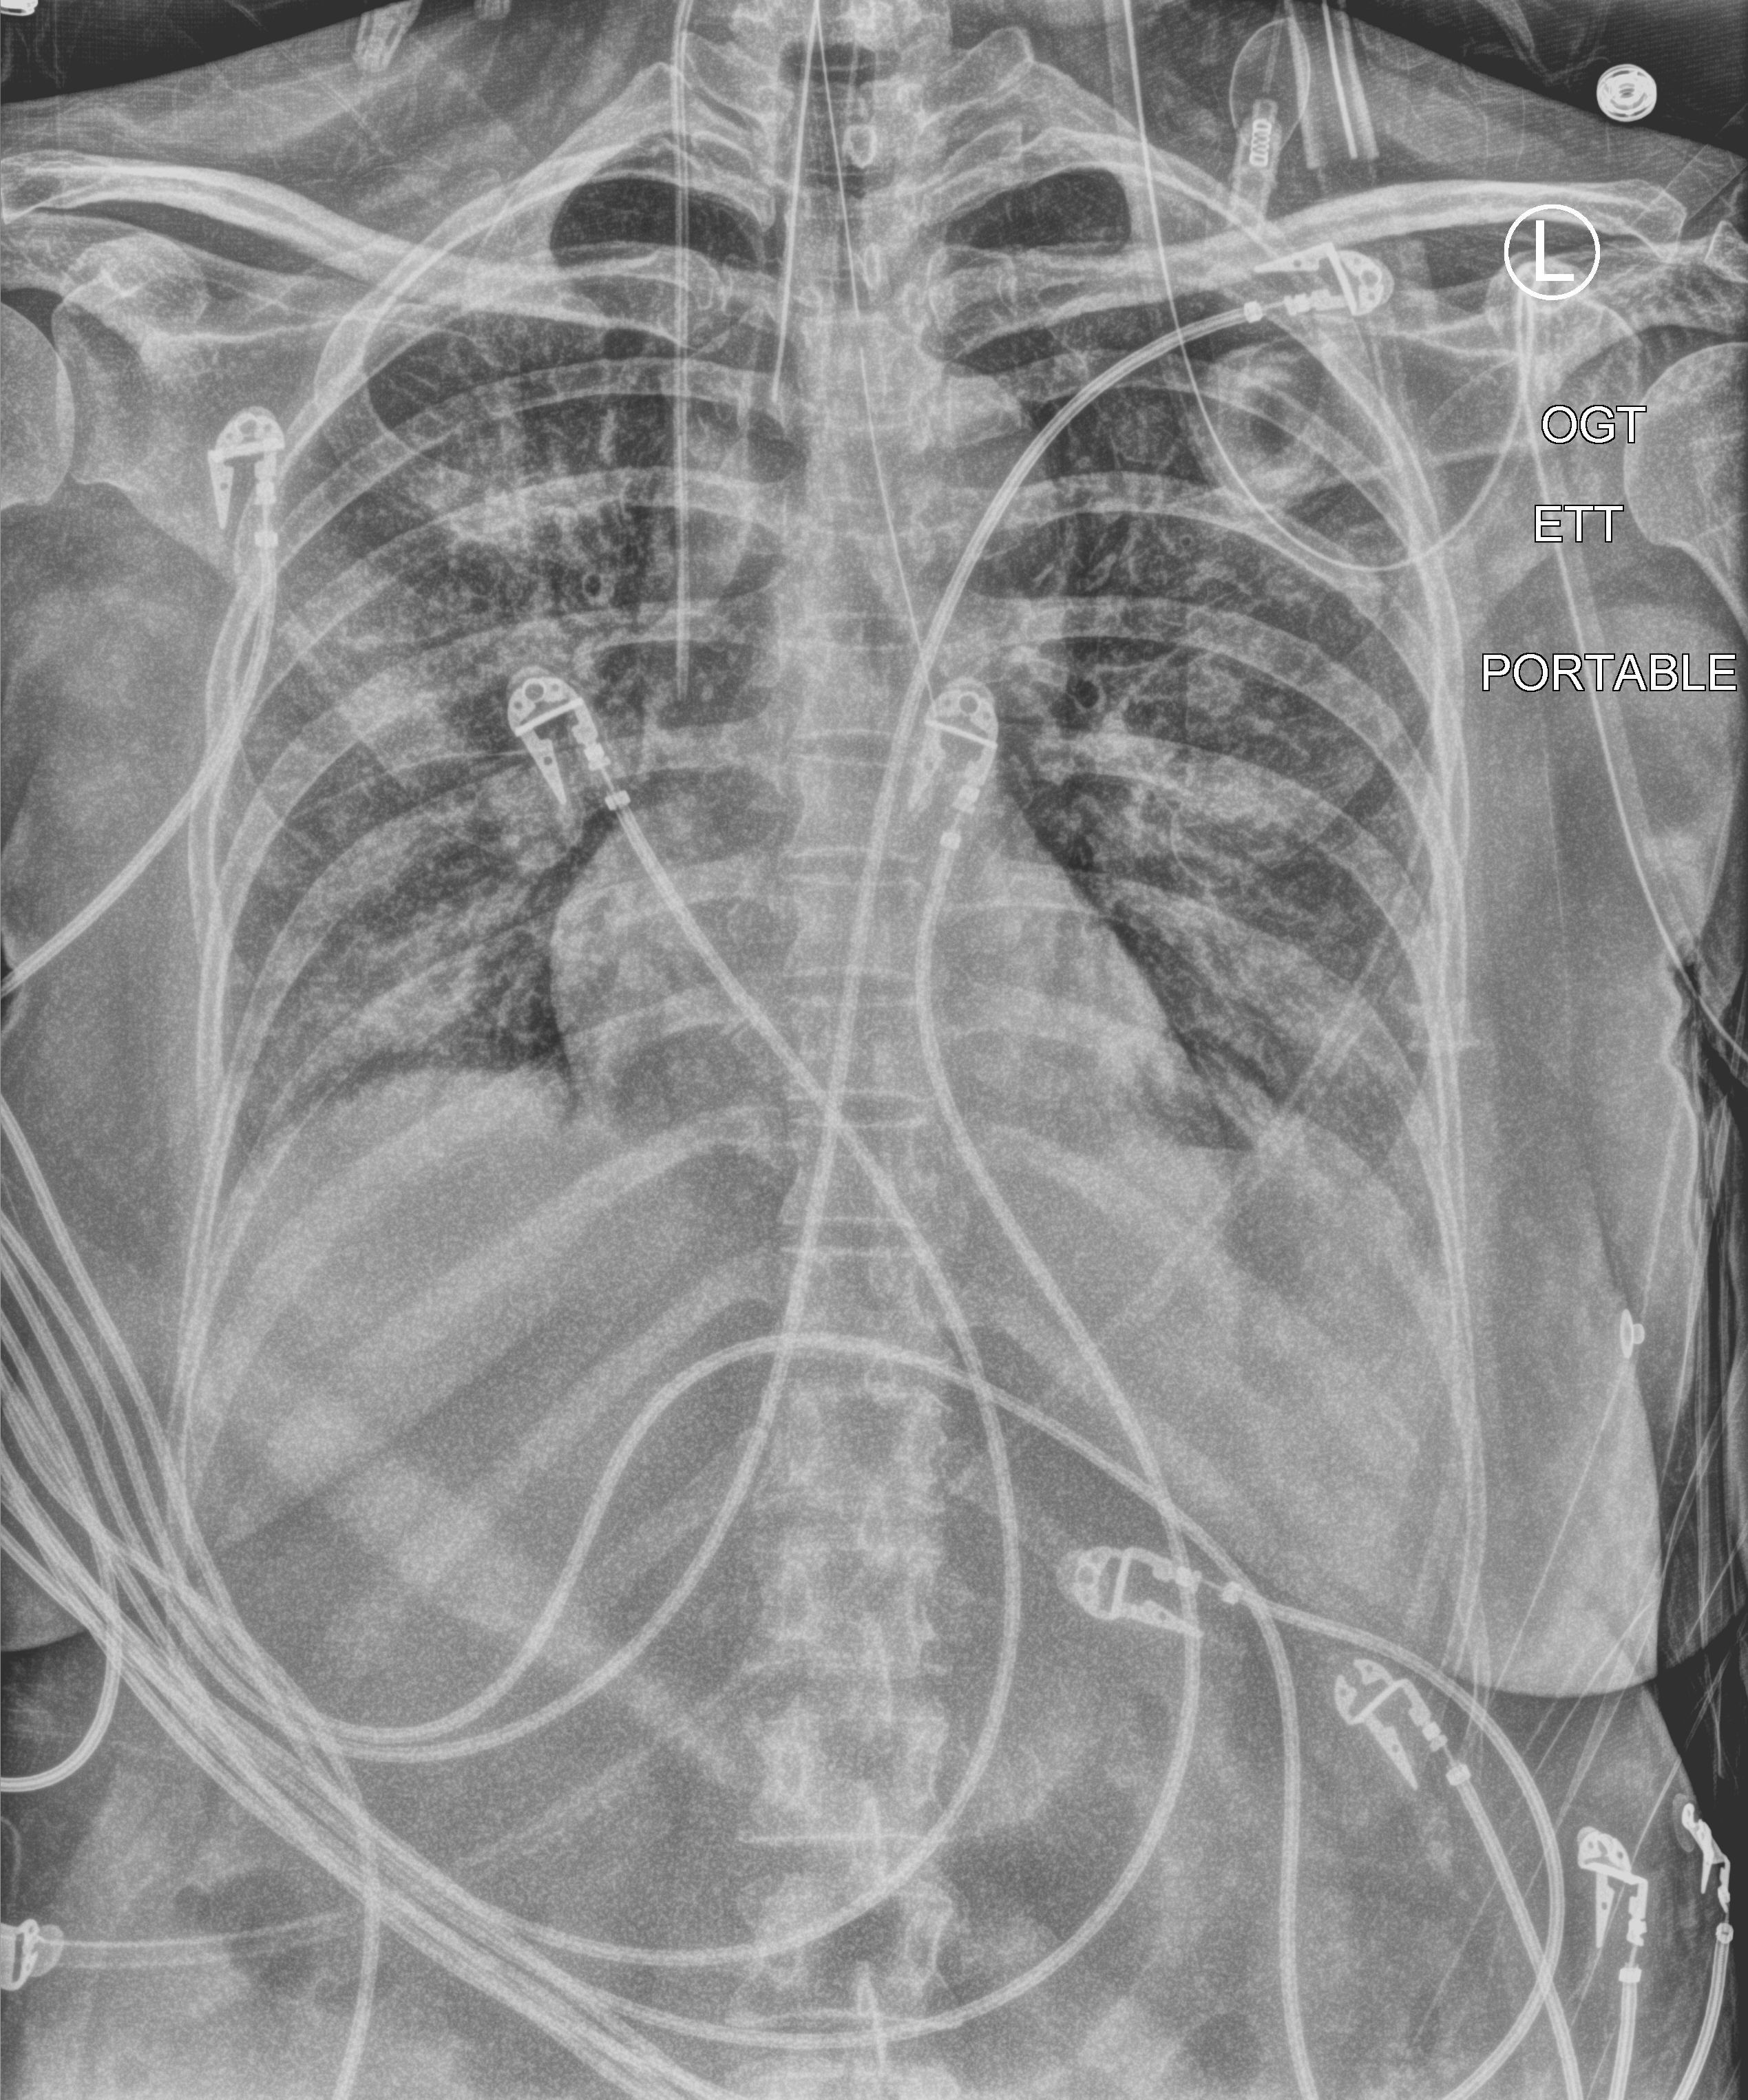
Portable chest radiograph; anteroposterior (AP) projection. Female patient hospitalised with COVID-19, age 18–59 years.
Hospital-stay facts (about this admission, not read from this image; timing relative to this image not recorded): admitted to intensive care during this hospital stay: yes.